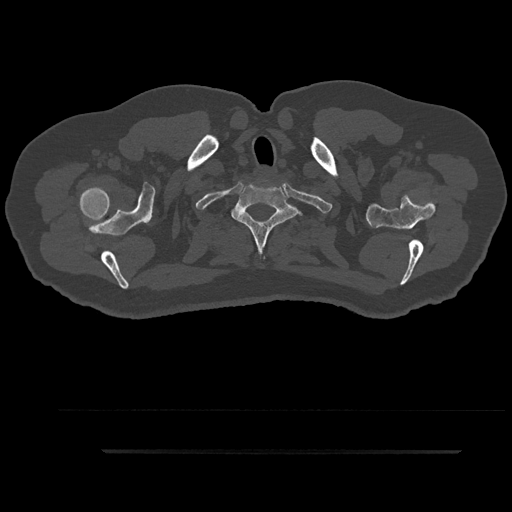
CT including the spine, one axial slice. Position 795 of 797 along the scan axis. 120 kVp. Bone window (W 1800 / L 400 HU). 512 × 512 image matrix, field of view 432 × 432 mm. Patient: male, 63 years. From the clinical record (not read from this slice): primary cancer: renal; vertebrae with lytic lesions (as recorded): T8.
Structures marked on this image (semi-automatic segmentation, software-assisted and operator-edited):
- T1 vertebra: bounding box <231,185,299,252> (left, top, right, bottom; pixels)
- T2 vertebra: <215,224,302,233>